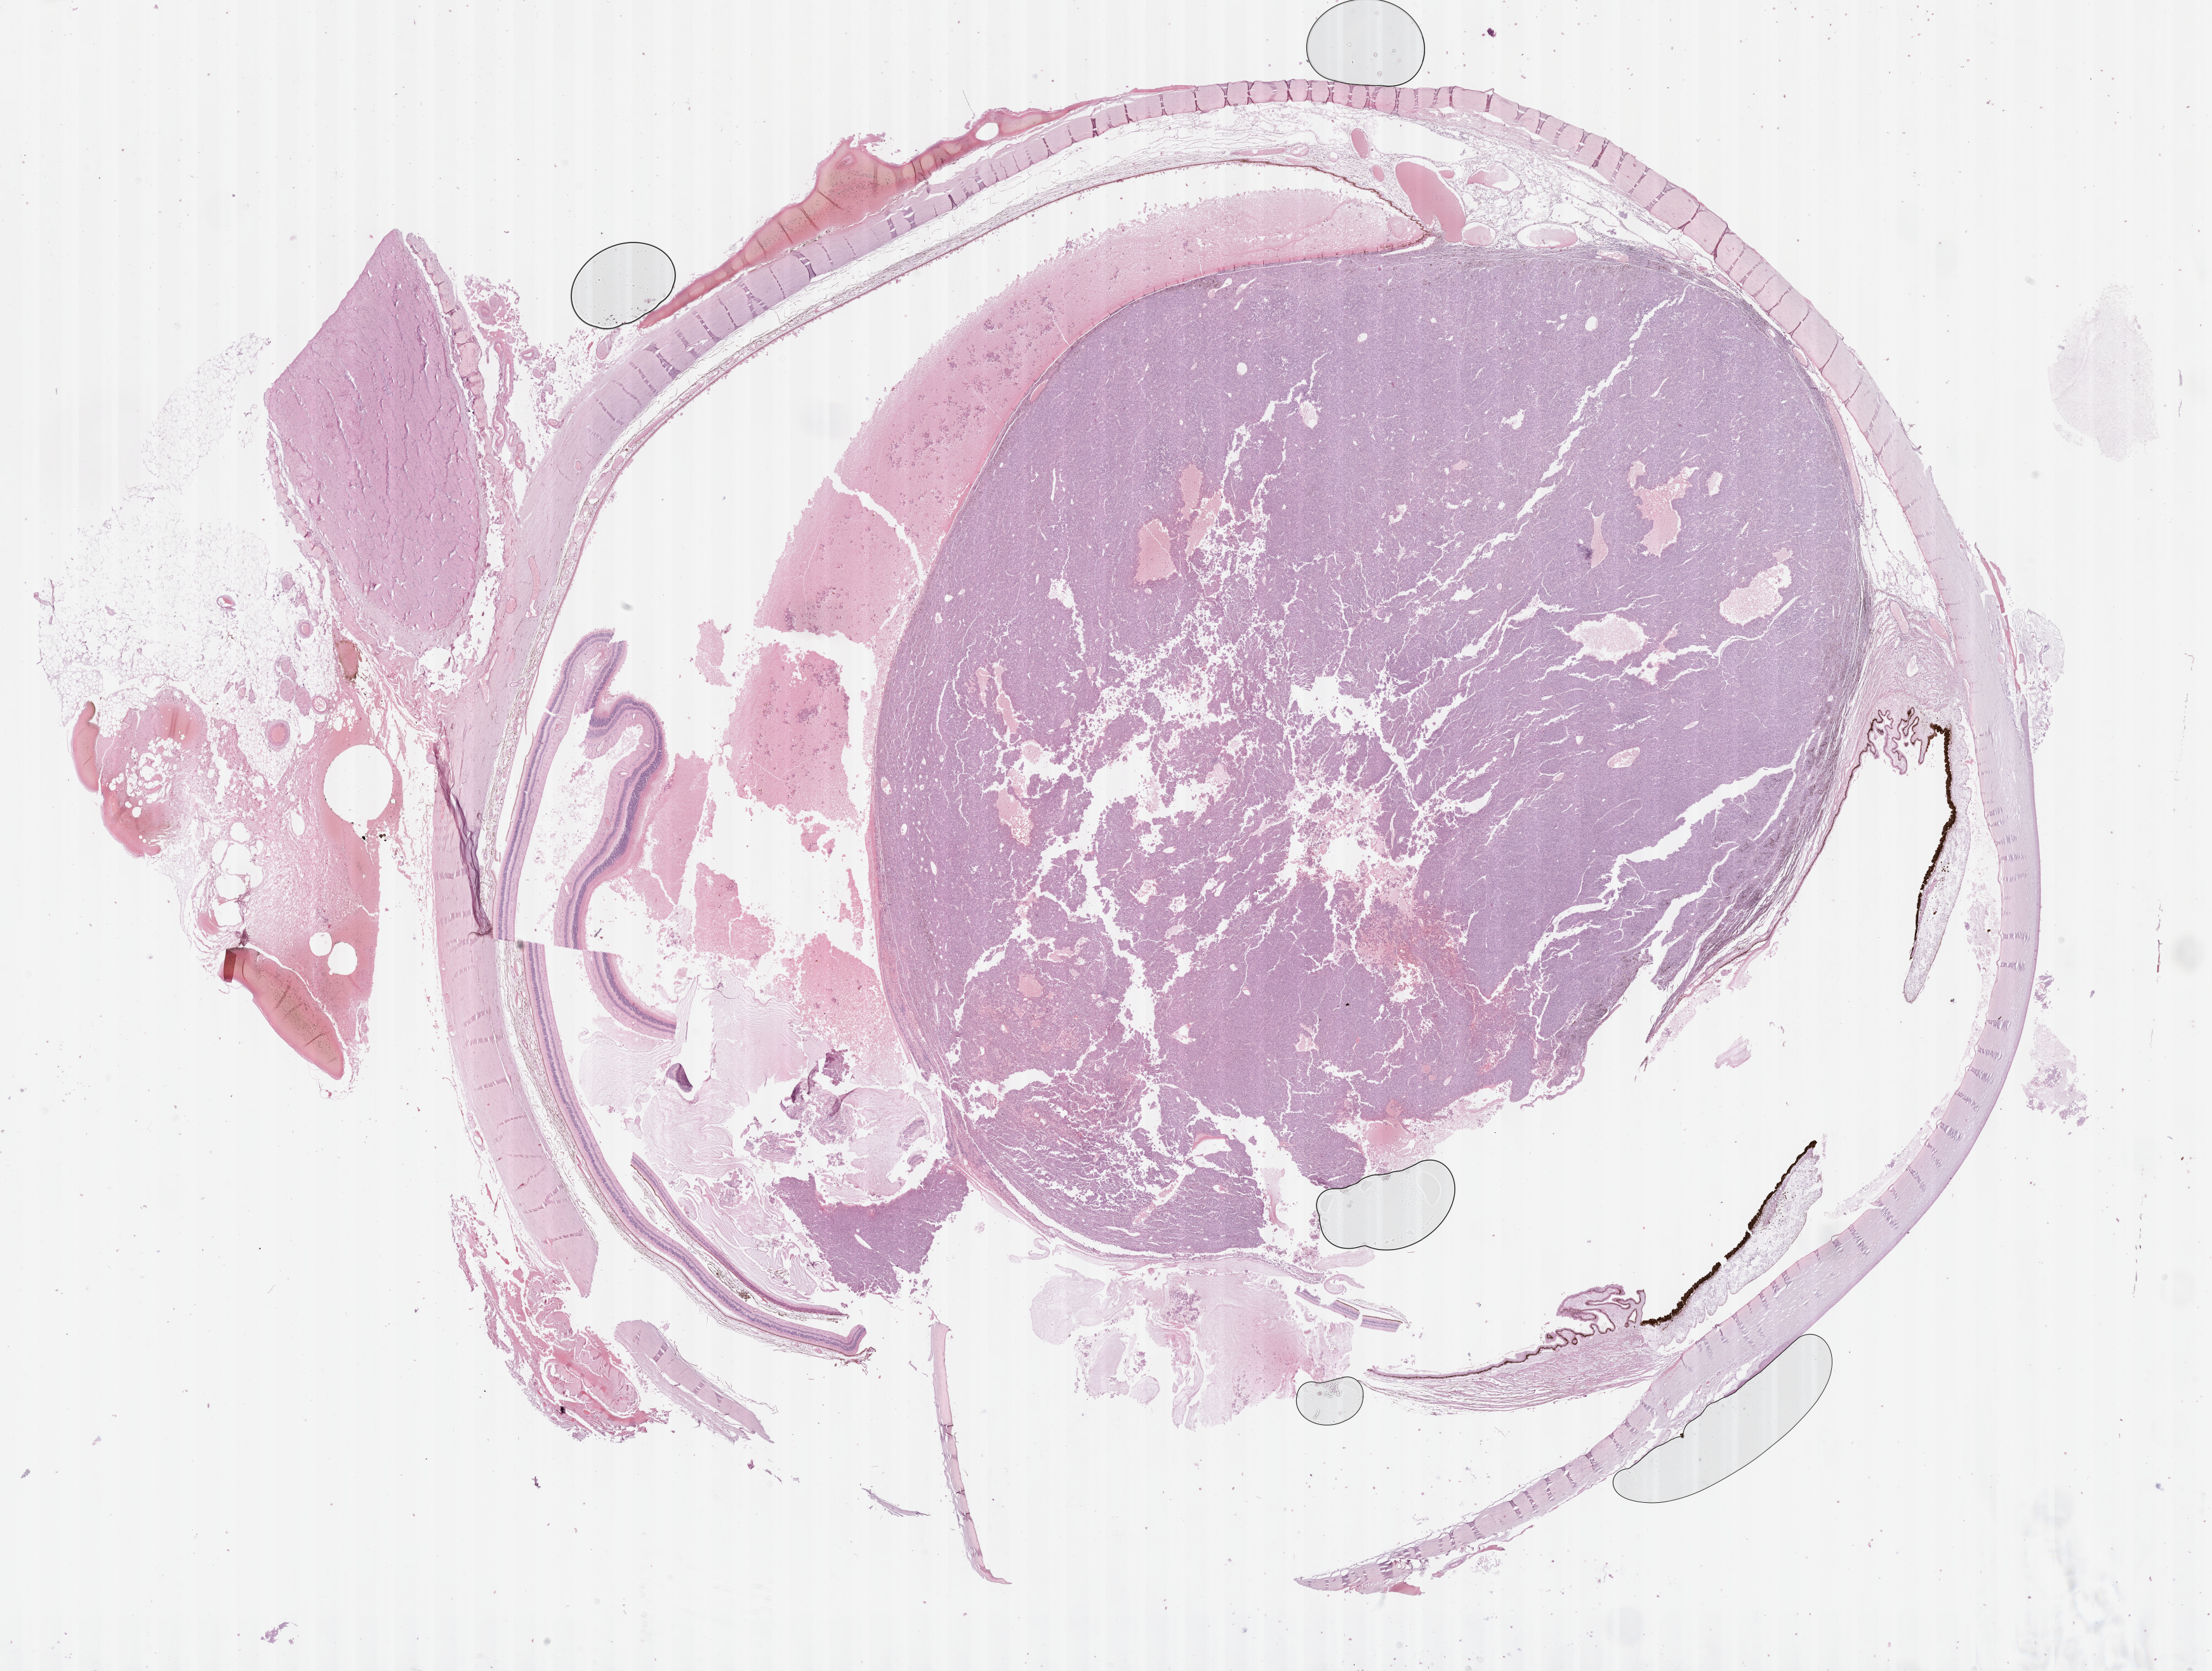
Digitized H&E-stained tissue section (whole slide) — a low-resolution overview of the entire scanned area, about 28.2 x 21.3 mm (acquisition: 40x scan); formalin-fixed paraffin-embedded (FFPE) diagnostic section; uvea, primary tumour sample. Female, age 49 years at initial diagnosis.
Laterality: left. AJCC pathologic stage: IIIA. Pathologic diagnosis: Epithelioid cell melanoma (choroid).